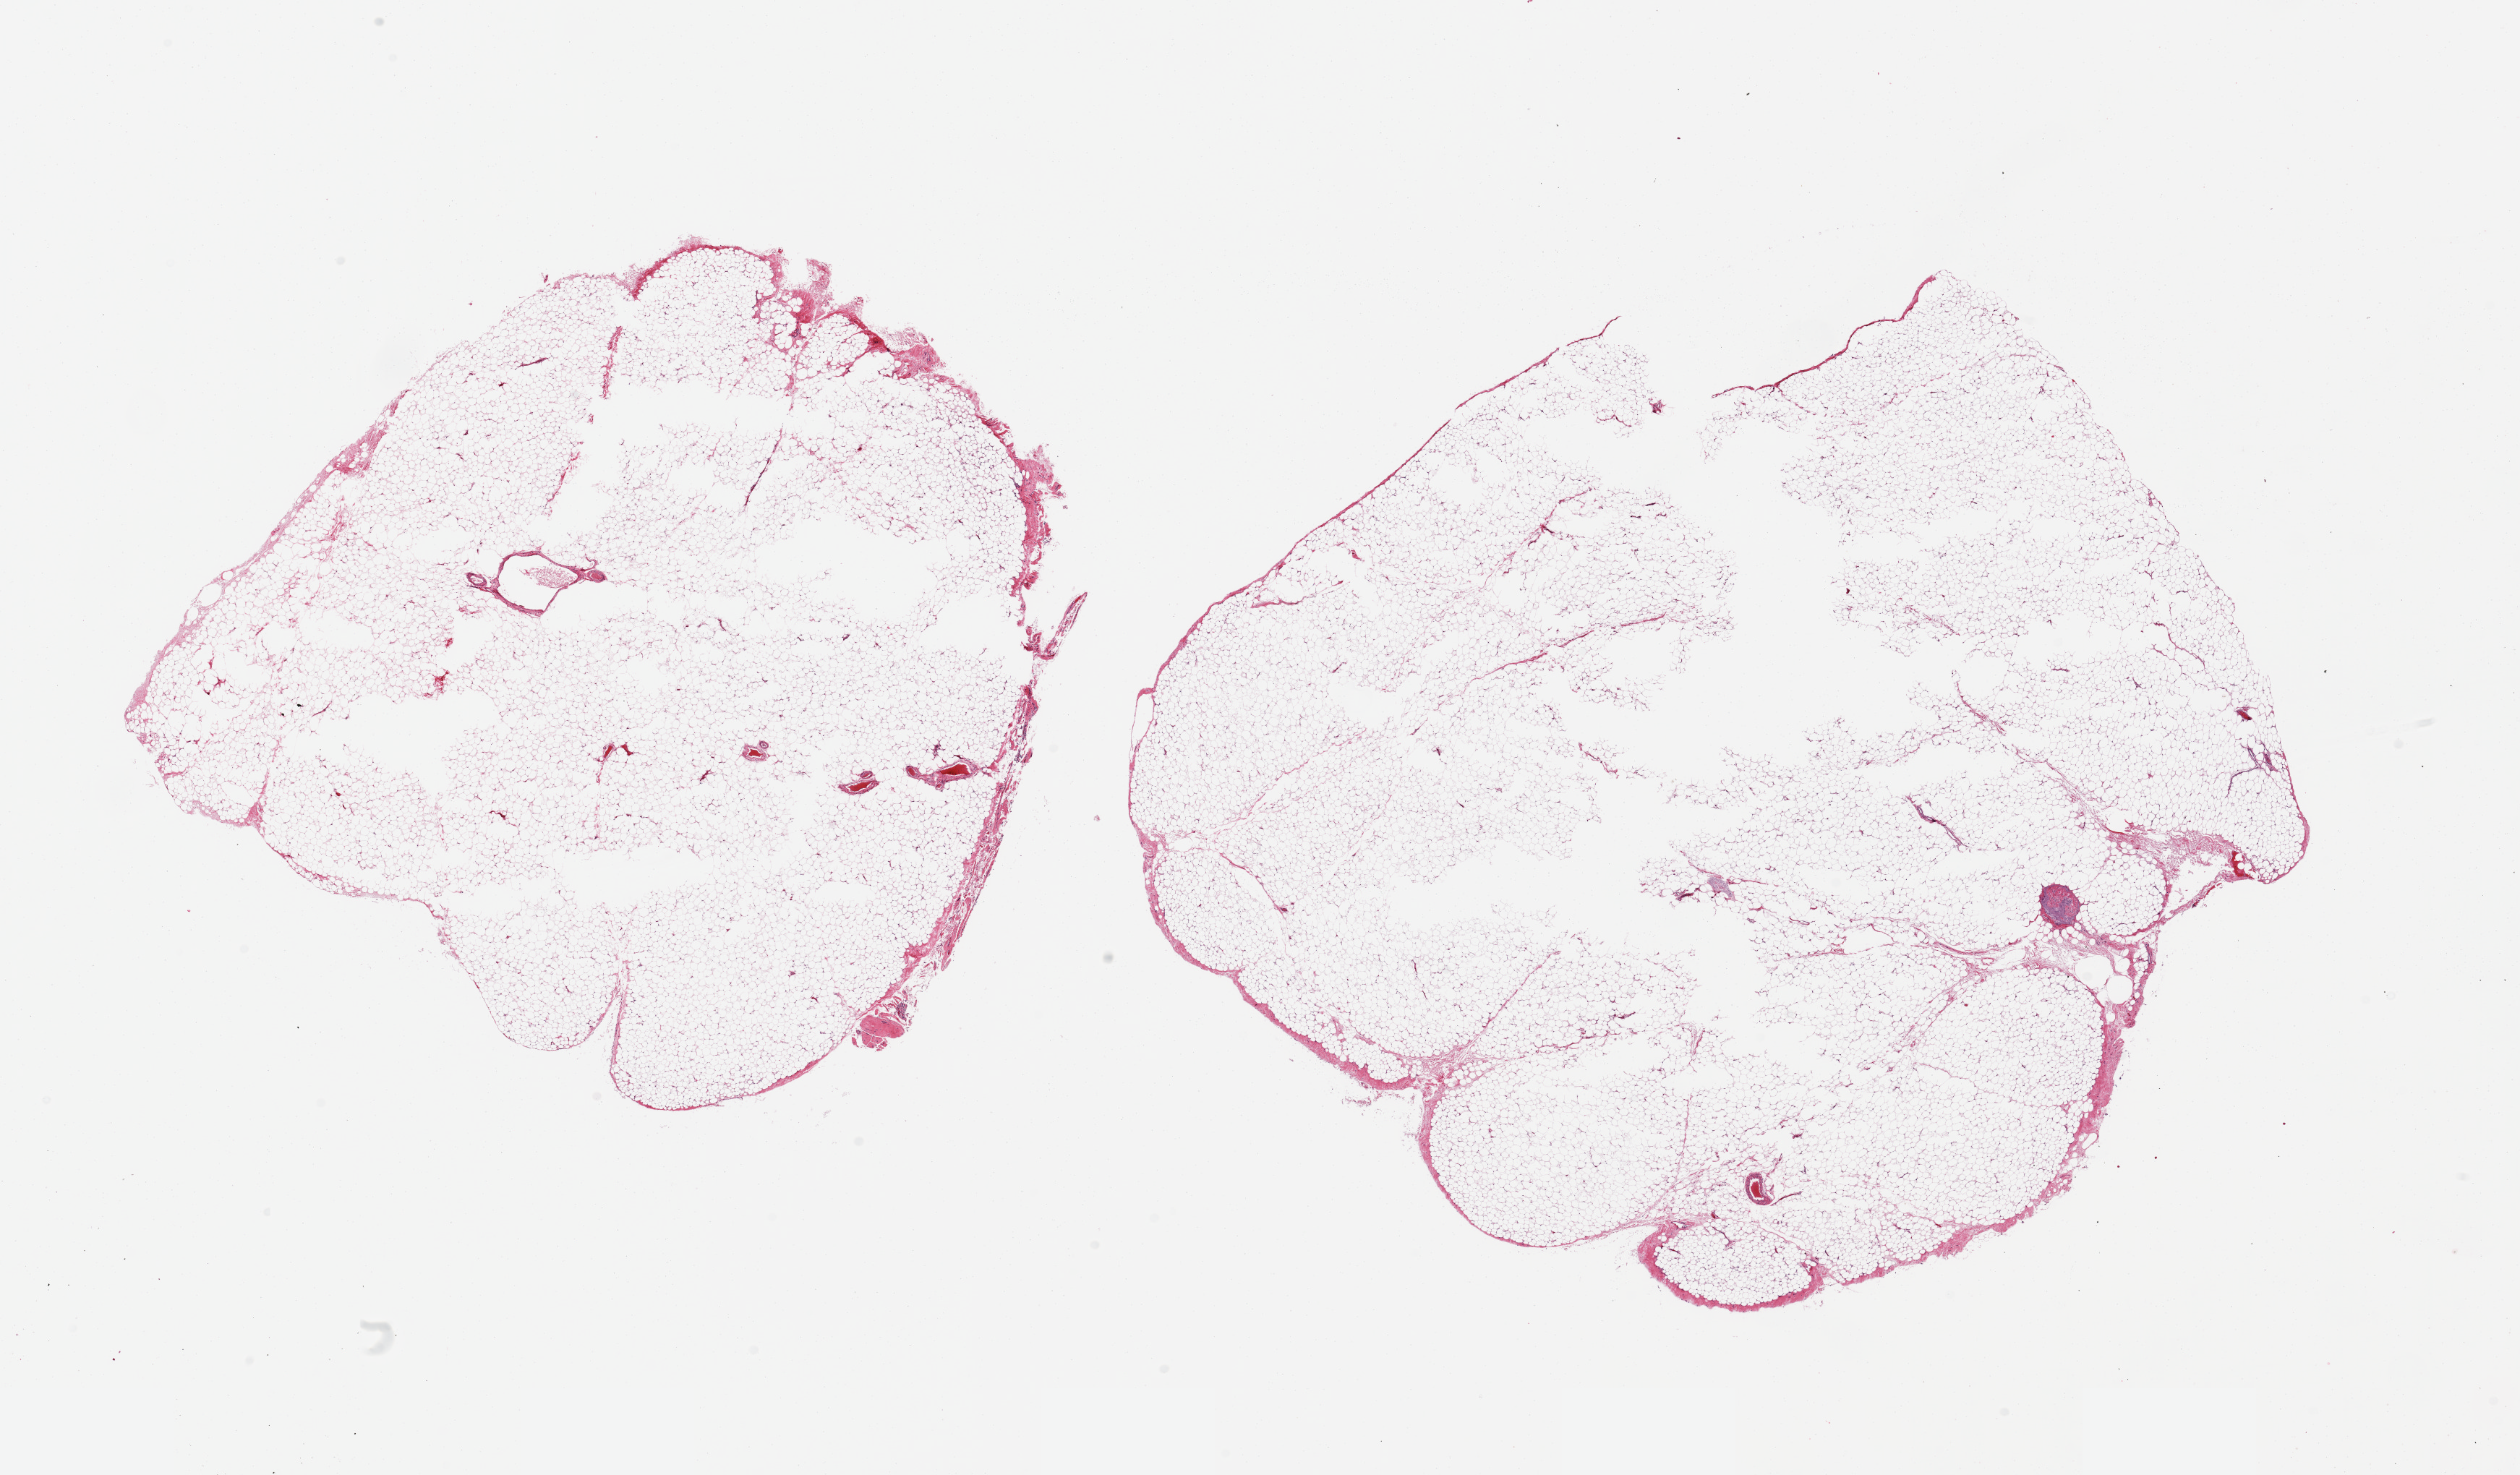
Digitized hematoxylin and eosin (H&E)-stained section — a low-resolution overview of the entire scanned area, about 27.6 x 16.1 mm; PAXgene-fixed paraffin-embedded (PFPE) section; section of omentum (target tissue); donor tissue sample. Male donor.
* review note (as recorded): 2 pieces; mature fat, central defects